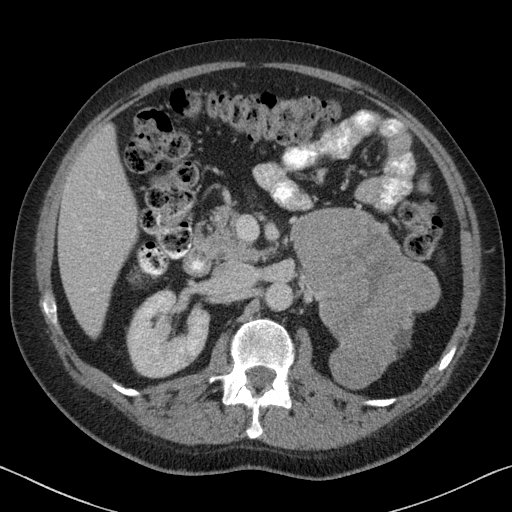
Contrast-enhanced abdominal CT, one axial slice. Position 40 of 88 along the scan axis. 120 kVp. Intravenous contrast given. Soft-tissue window (W 400 / L 40 HU). 3 mm slice thickness. 512 × 512 image matrix. Patient: male, 51 years. Case-level facts recorded for this patient, not image findings: diagnosis: adrenocortical carcinoma; tumour side: left adrenal; tumour size at pathology: 16.5 cm; Ki-67 index: 30 %; stage (as recorded): 2.
Structures marked on this image (semi-automatically segmented with operator editing):
- mass: bounding box [x1, y1, x2, y2] px = [290, 208, 438, 387]